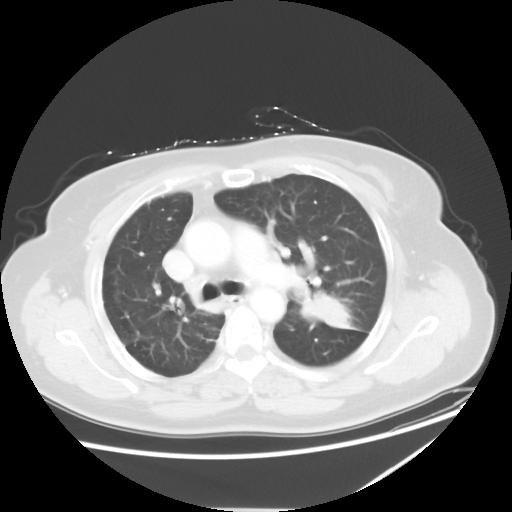
Chest CT, one axial slice; position 36 of 54 along the scan axis; reconstruction kernel STANDARD; 120 kVp; lung window (W 1500 / L -600 HU); 5 mm slice thickness; 512 × 512 image matrix, field of view 384 × 384 mm. Female patient, age 61 years. Case-level facts recorded for this patient, not image findings: clinical TNM (as recorded): T1c N3 M1.
Annotated regions visible in this slice (bounding box drawn by a radiologist):
- lung tumour (recorded histology: adenocarcinoma): bounding box <295,291,368,335> (left, top, right, bottom; pixels)